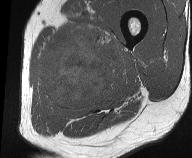
MRI of an extremity soft-tissue mass, one axial slice; position 20 of 61 along the scan axis; MR volume resampled by the dataset authors to the PET/CT grid (not the native acquisition matrix); 3.27 mm slice thickness; 192 × 158 image matrix, field of view 187 × 154 mm. Male patient. From the clinical record (not read from this slice): histological type: pleiomorphic liposarcoma; grade: high; site of the primary tumour: left thigh.
Outlined on this slice (expert contour drawn on MRI and transferred to this co-registered scan by the dataset authors):
- gross tumour volume including surrounding oedema: box from (x=36, y=23) to (x=126, y=115) px
- gross tumour volume (mass): (x=41, y=34)–(x=112, y=109)